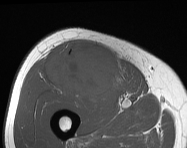
MRI of an extremity soft-tissue mass, one axial slice. Slice 77 of 114 in the series (ordered by position). MR volume resampled by the dataset authors to the PET/CT grid (not the native acquisition matrix). 3.27 mm slice thickness. 187 × 148 image matrix, field of view 183 × 145 mm. Male patient. From the clinical record (not read from this slice): histological type: pleiomorphic leiomyosarcoma; grade: intermediate; site of the primary tumour: right thigh.
Annotated regions visible in this slice (expert contour drawn on MRI and transferred to this co-registered scan by the dataset authors):
- gross tumour volume including surrounding oedema: box from (x=47, y=43) to (x=122, y=99) px
- gross tumour volume (mass): (x=47, y=43)–(x=122, y=99)